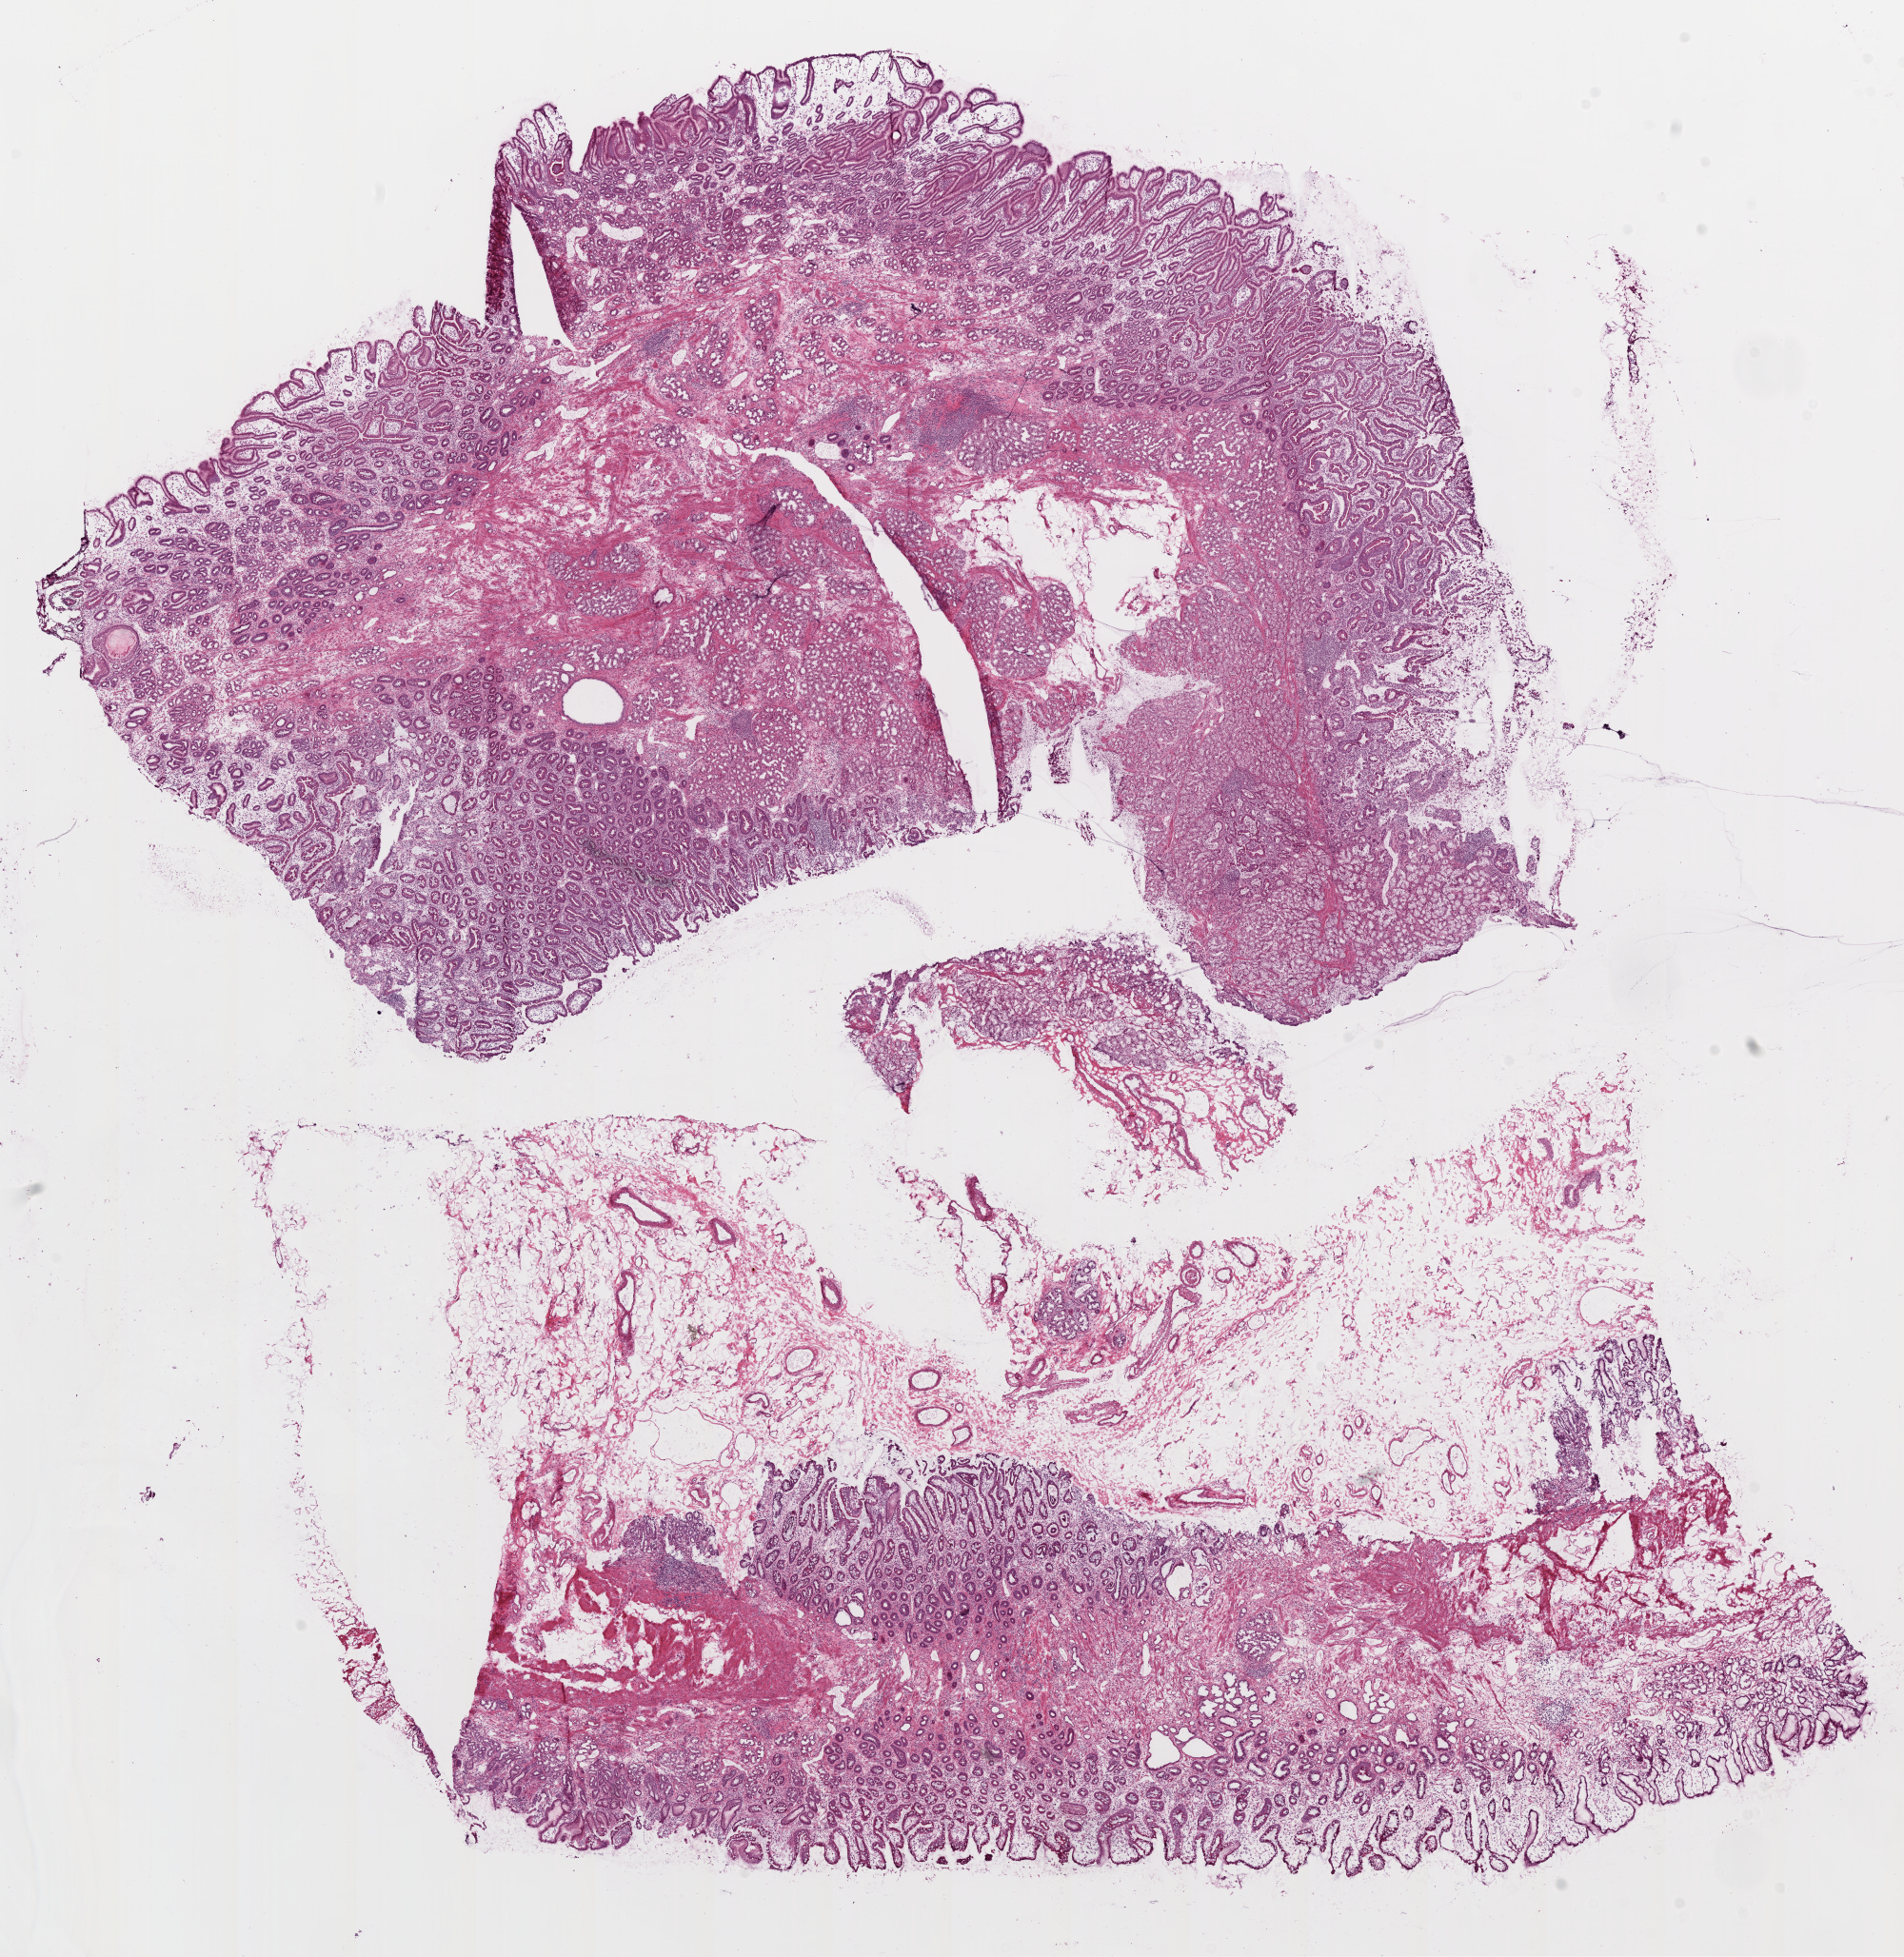
Whole-slide histology image, H&E-stained — whole scanned area (about 16.0 x 16.5 mm) shown as a low-resolution overview, frozen section from the top of the tissue portion, sample: solid tissue normal (non-tumour tissue), stomach. Female patient; age at initial diagnosis 76 years.
This section: solid tissue normal sample (biorepository sample class). Patient diagnosis: Adenocarcinoma, NOS.